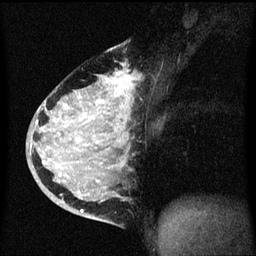
Breast MRI (dynamic contrast-enhanced), one sagittal slice. Dynamic contrast-enhanced series, image 2 of 3 at this slice position (ordered by acquisition). 1.5 T. TE 4.2 ms, TR 8.4 ms. 256 × 256 image matrix. Female patient, age 34 years. From the clinical record (not read from this slice): setting: breast cancer imaged before/during neoadjuvant chemotherapy; receptor status: HR-positive, HER2-negative.
Annotated regions visible in this slice (semi-automatic segmentation, software-assisted and operator-edited):
- analysis volume of interest (the breast-tissue region the enhancement analysis was run in; not a lesion): bounding box <34,48,131,215> (left, top, right, bottom; pixels)
- tumour enhancement mask (voxels above the 70 % enhancement threshold inside the analysis volume of interest): <36,80,127,213>